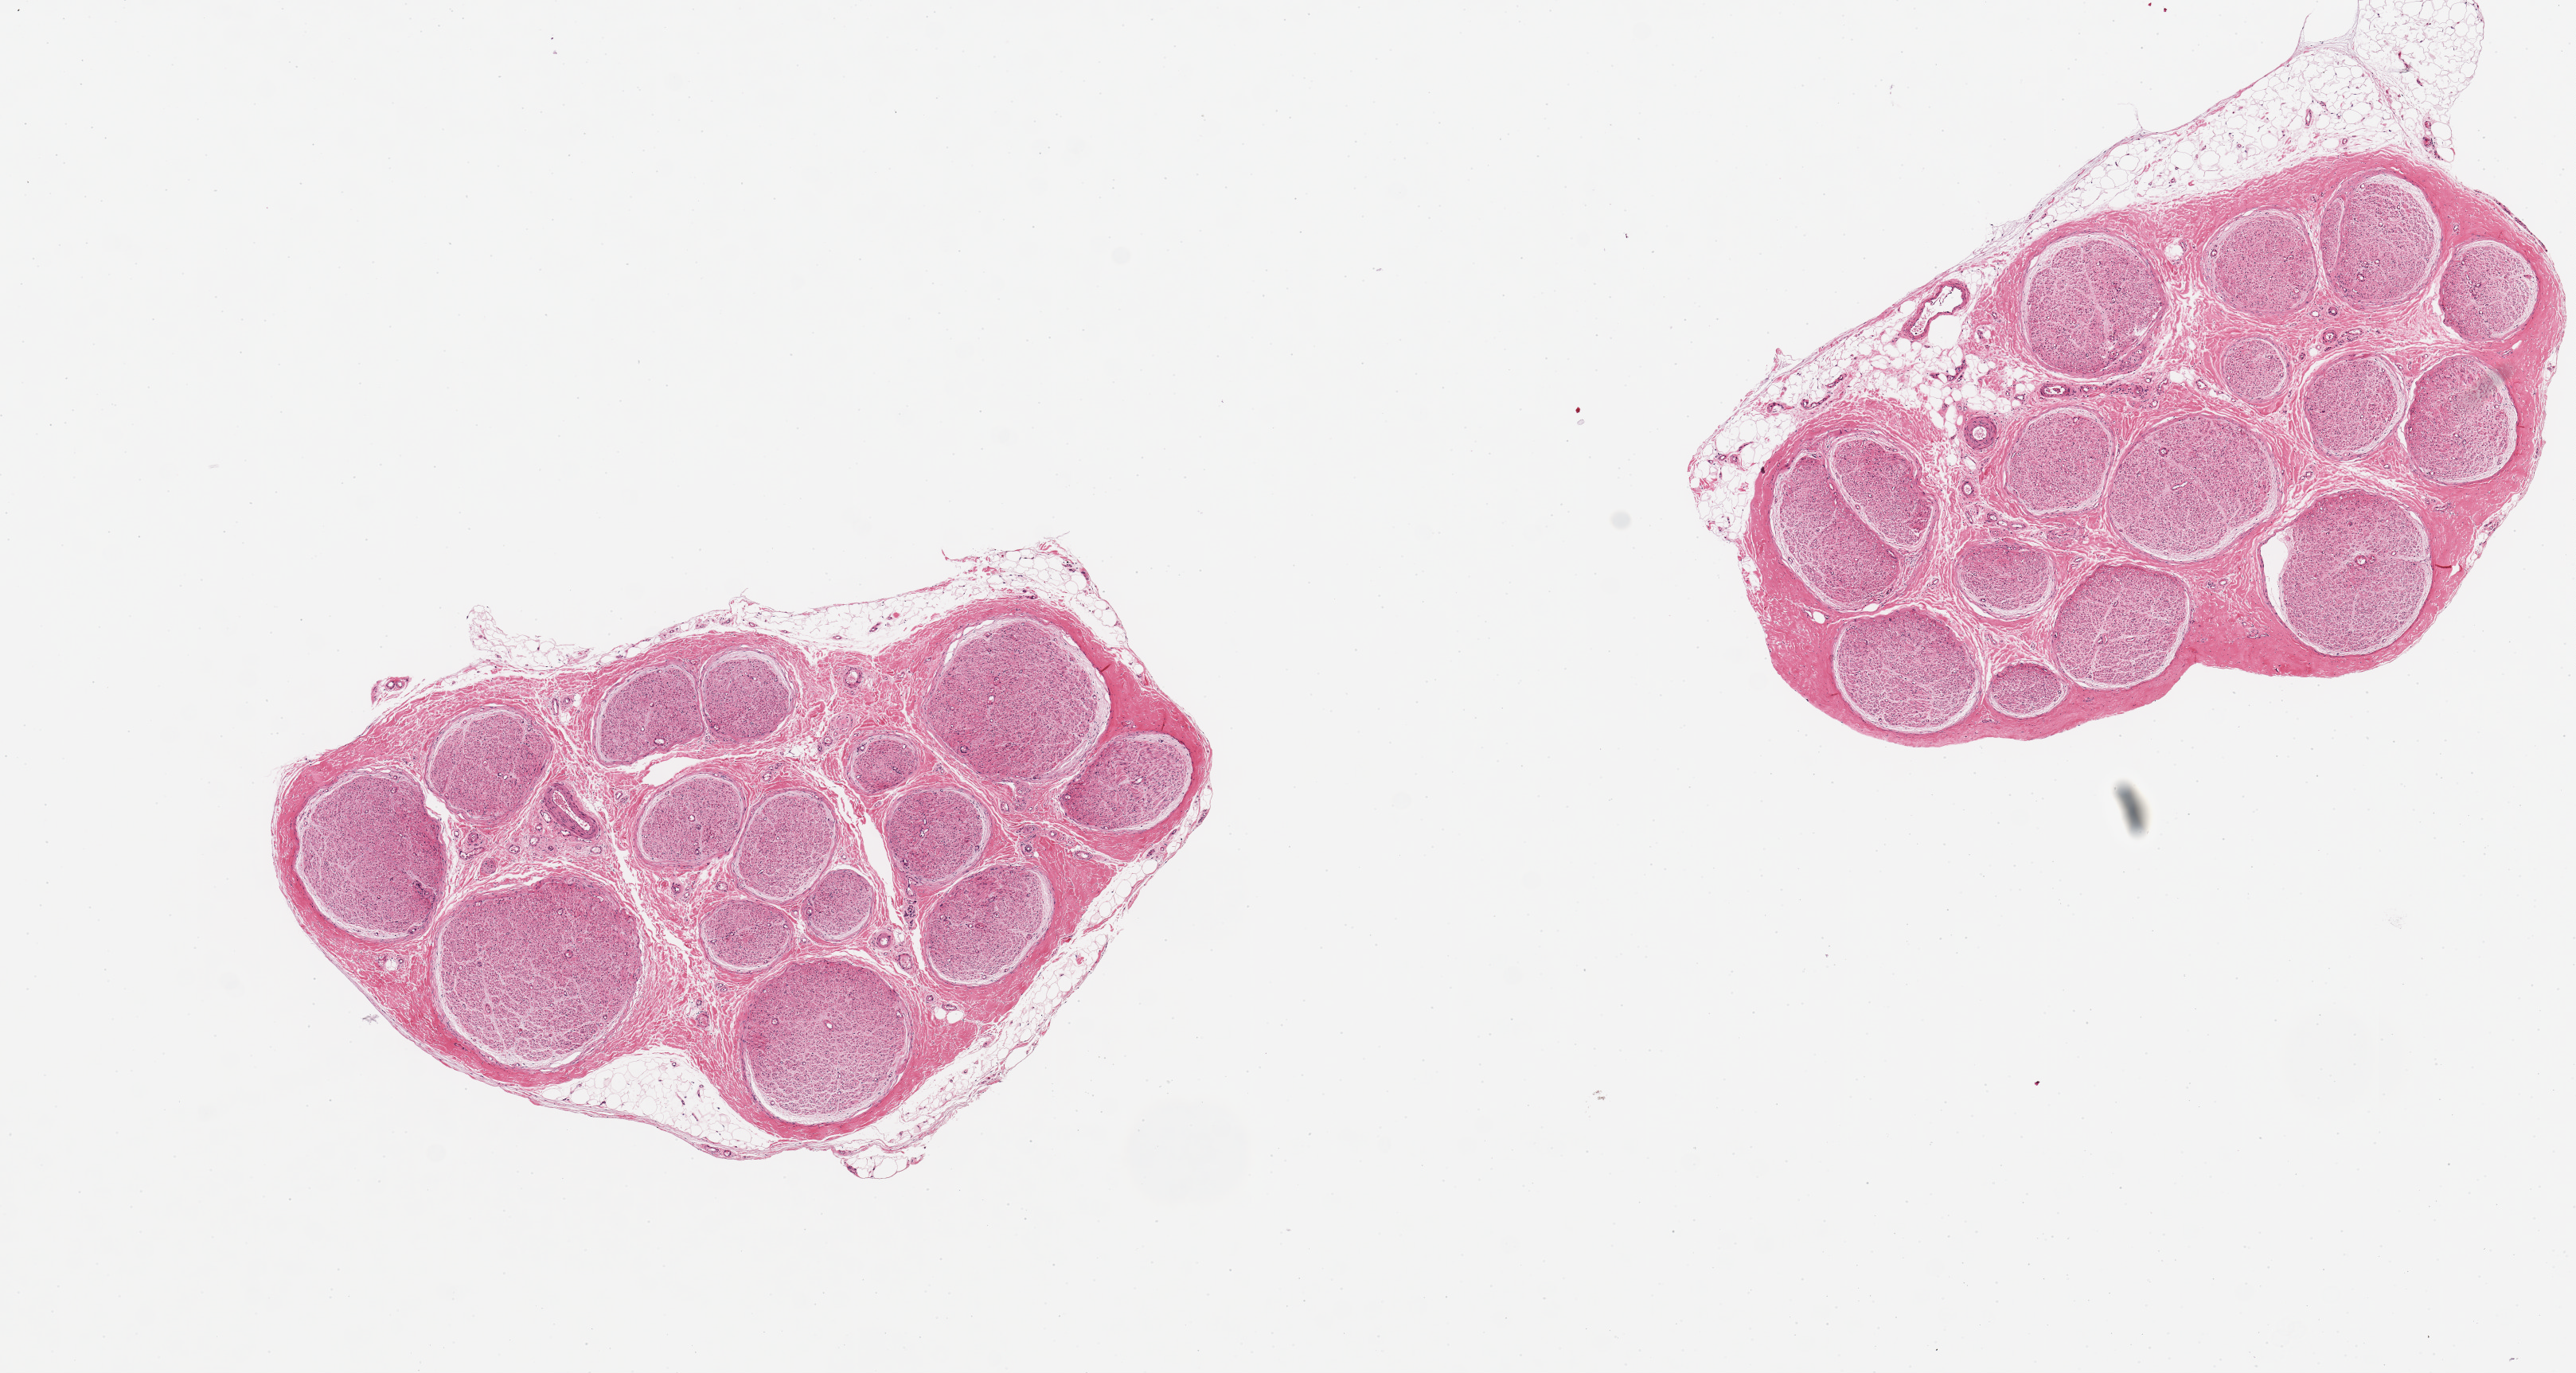
Whole-slide image, haematoxylin and eosin stain, low-resolution overview of the scanned area, about 12.8 x 6.8 mm, PAXgene-fixed, paraffin-embedded tissue, section of tibial nerve (target tissue), donor tissue sample. Donor: male.
- review note (as recorded): 2 aliquots, ~4.5x2.5. Adherent nubbine of fat, ~2x0.5mm on one